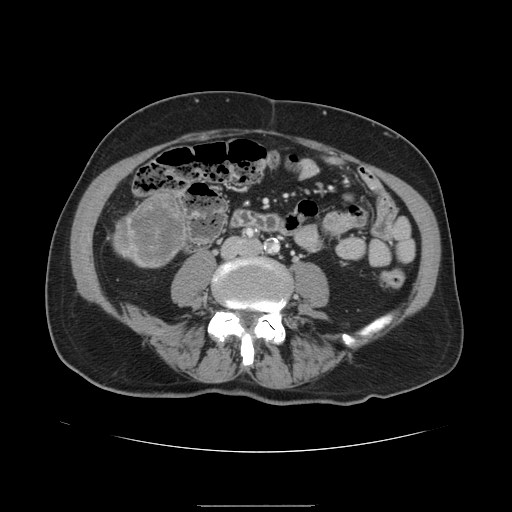
Contrast-enhanced abdominal CT, one axial slice. Slice 15 of 168 in the series (ordered by position). Intravenous contrast given. Soft-tissue window (W 400 / L 40 HU). 512 × 512 image matrix, field of view 386 × 386 mm. Male patient, age 74 years. Case-level facts recorded for this patient, not image findings: diagnosis: colorectal cancer liver metastases, imaged before liver resection; multiple liver metastases: no; largest metastasis: 14.5 cm; chemotherapy before resection: no.
Outlined on this slice (outlined manually by an expert reader):
- liver: bounding box <114,190,190,268> (left, top, right, bottom; pixels)
- liver metastasis: <119,194,186,265>